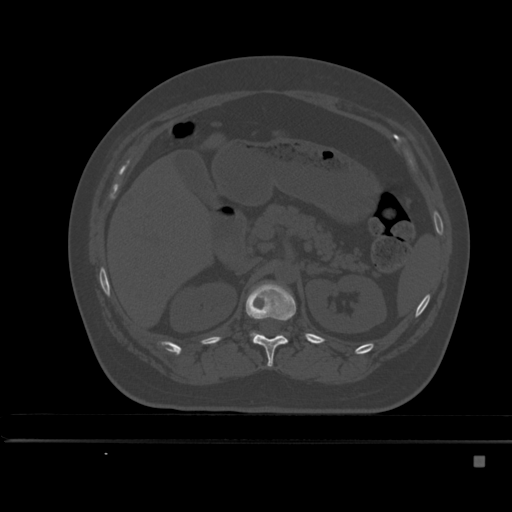
CT including the spine, one axial slice. Position 208 of 495 along the scan axis. Bone window (W 1800 / L 400 HU). 1.5 mm slice thickness. 512 × 512 image matrix, field of view 404 × 404 mm. Female patient, age 33 years. From the clinical record (not read from this slice): primary cancer: breast; vertebrae with lytic lesions (as recorded): T1.
Outlined on this slice (semi-automatically segmented with operator editing):
- L1 vertebra: bounding box [x1, y1, x2, y2] px = [251, 332, 257, 339]
- T12 vertebra: [246, 282, 296, 367]